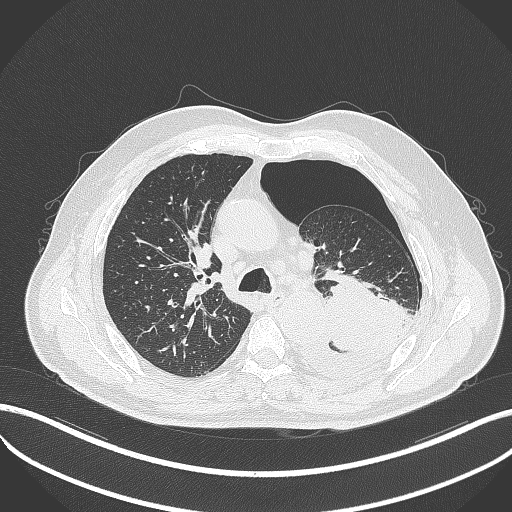
Chest CT, one axial slice; position 347 of 464 along the scan axis; lung window (W 1500 / L -600 HU); 1 mm slice thickness; 512 × 512 image matrix, field of view 400 × 400 mm. Male patient, age 76 years. Case-level facts recorded for this patient, not image findings: clinical TNM (as recorded): T3 N0 M1b.
Outlined on this slice (rectangle marked by the reading radiologist):
- lung tumour (recorded histology: adenocarcinoma): box from (x=320, y=267) to (x=407, y=350) px